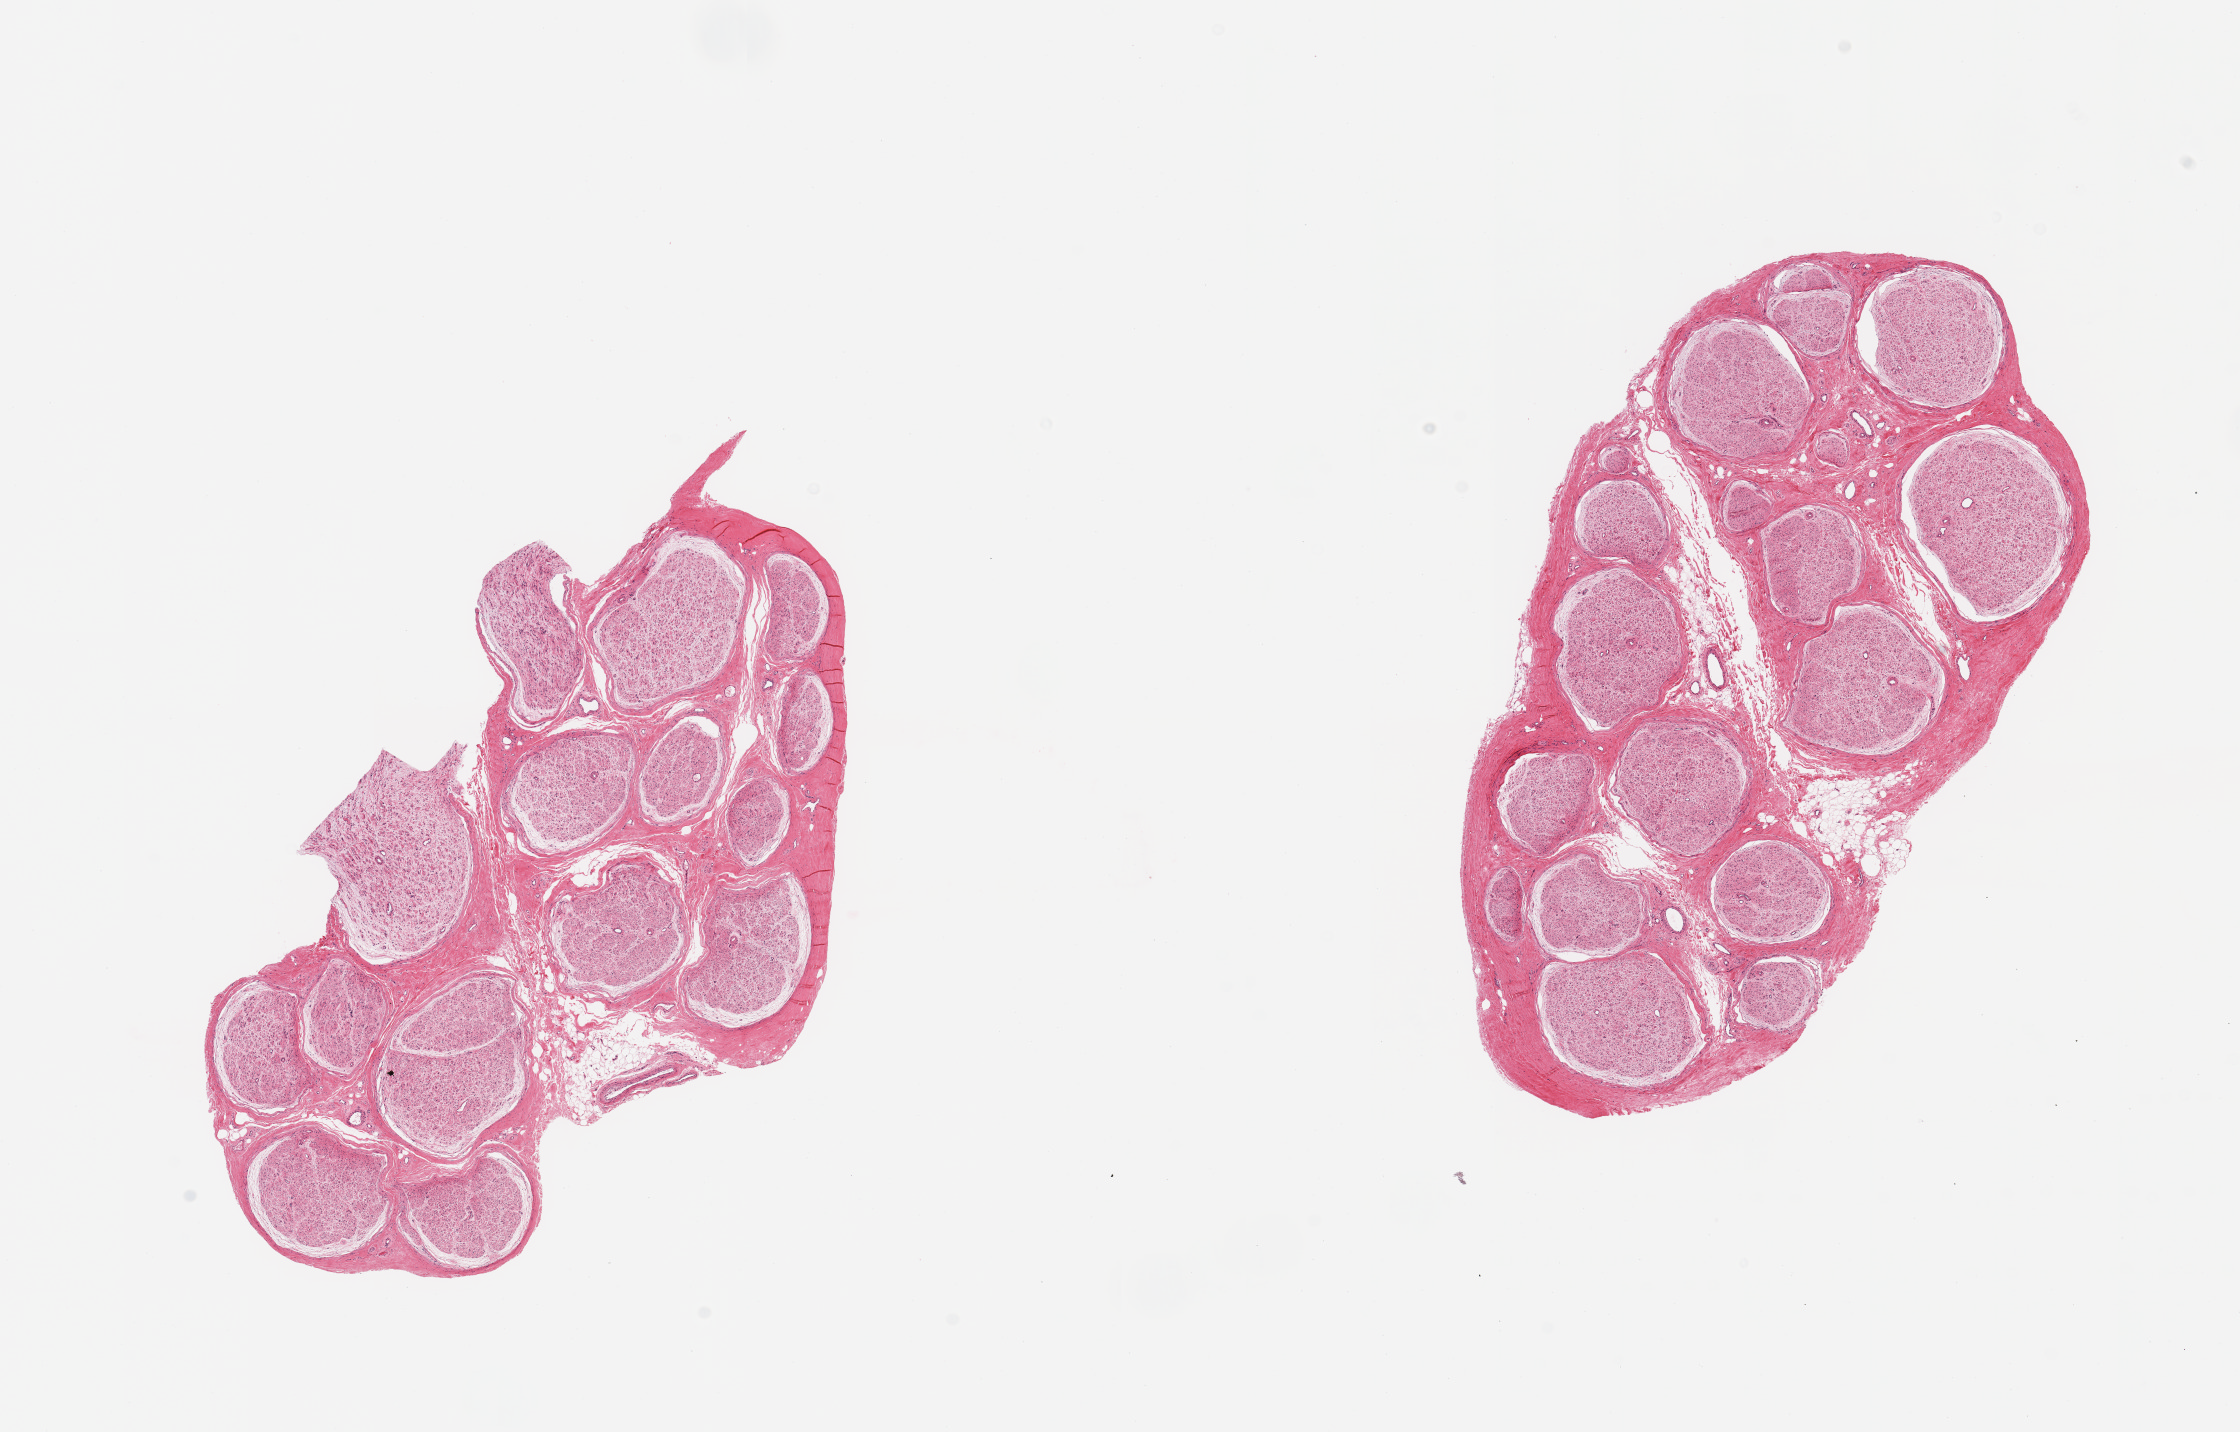
Digitized hematoxylin and eosin (H&E)-stained section, whole scanned area (about 17.7 x 11.3 mm, acquisition: 20x scan) shown as a low-resolution overview, PAXgene-fixed paraffin-embedded (PFPE) section, target tissue: tibial nerve, tissue donor sample. Male donor.
Pathologist's review note for this sample: 2 pieces; nerve with minimal attached and internal fat.